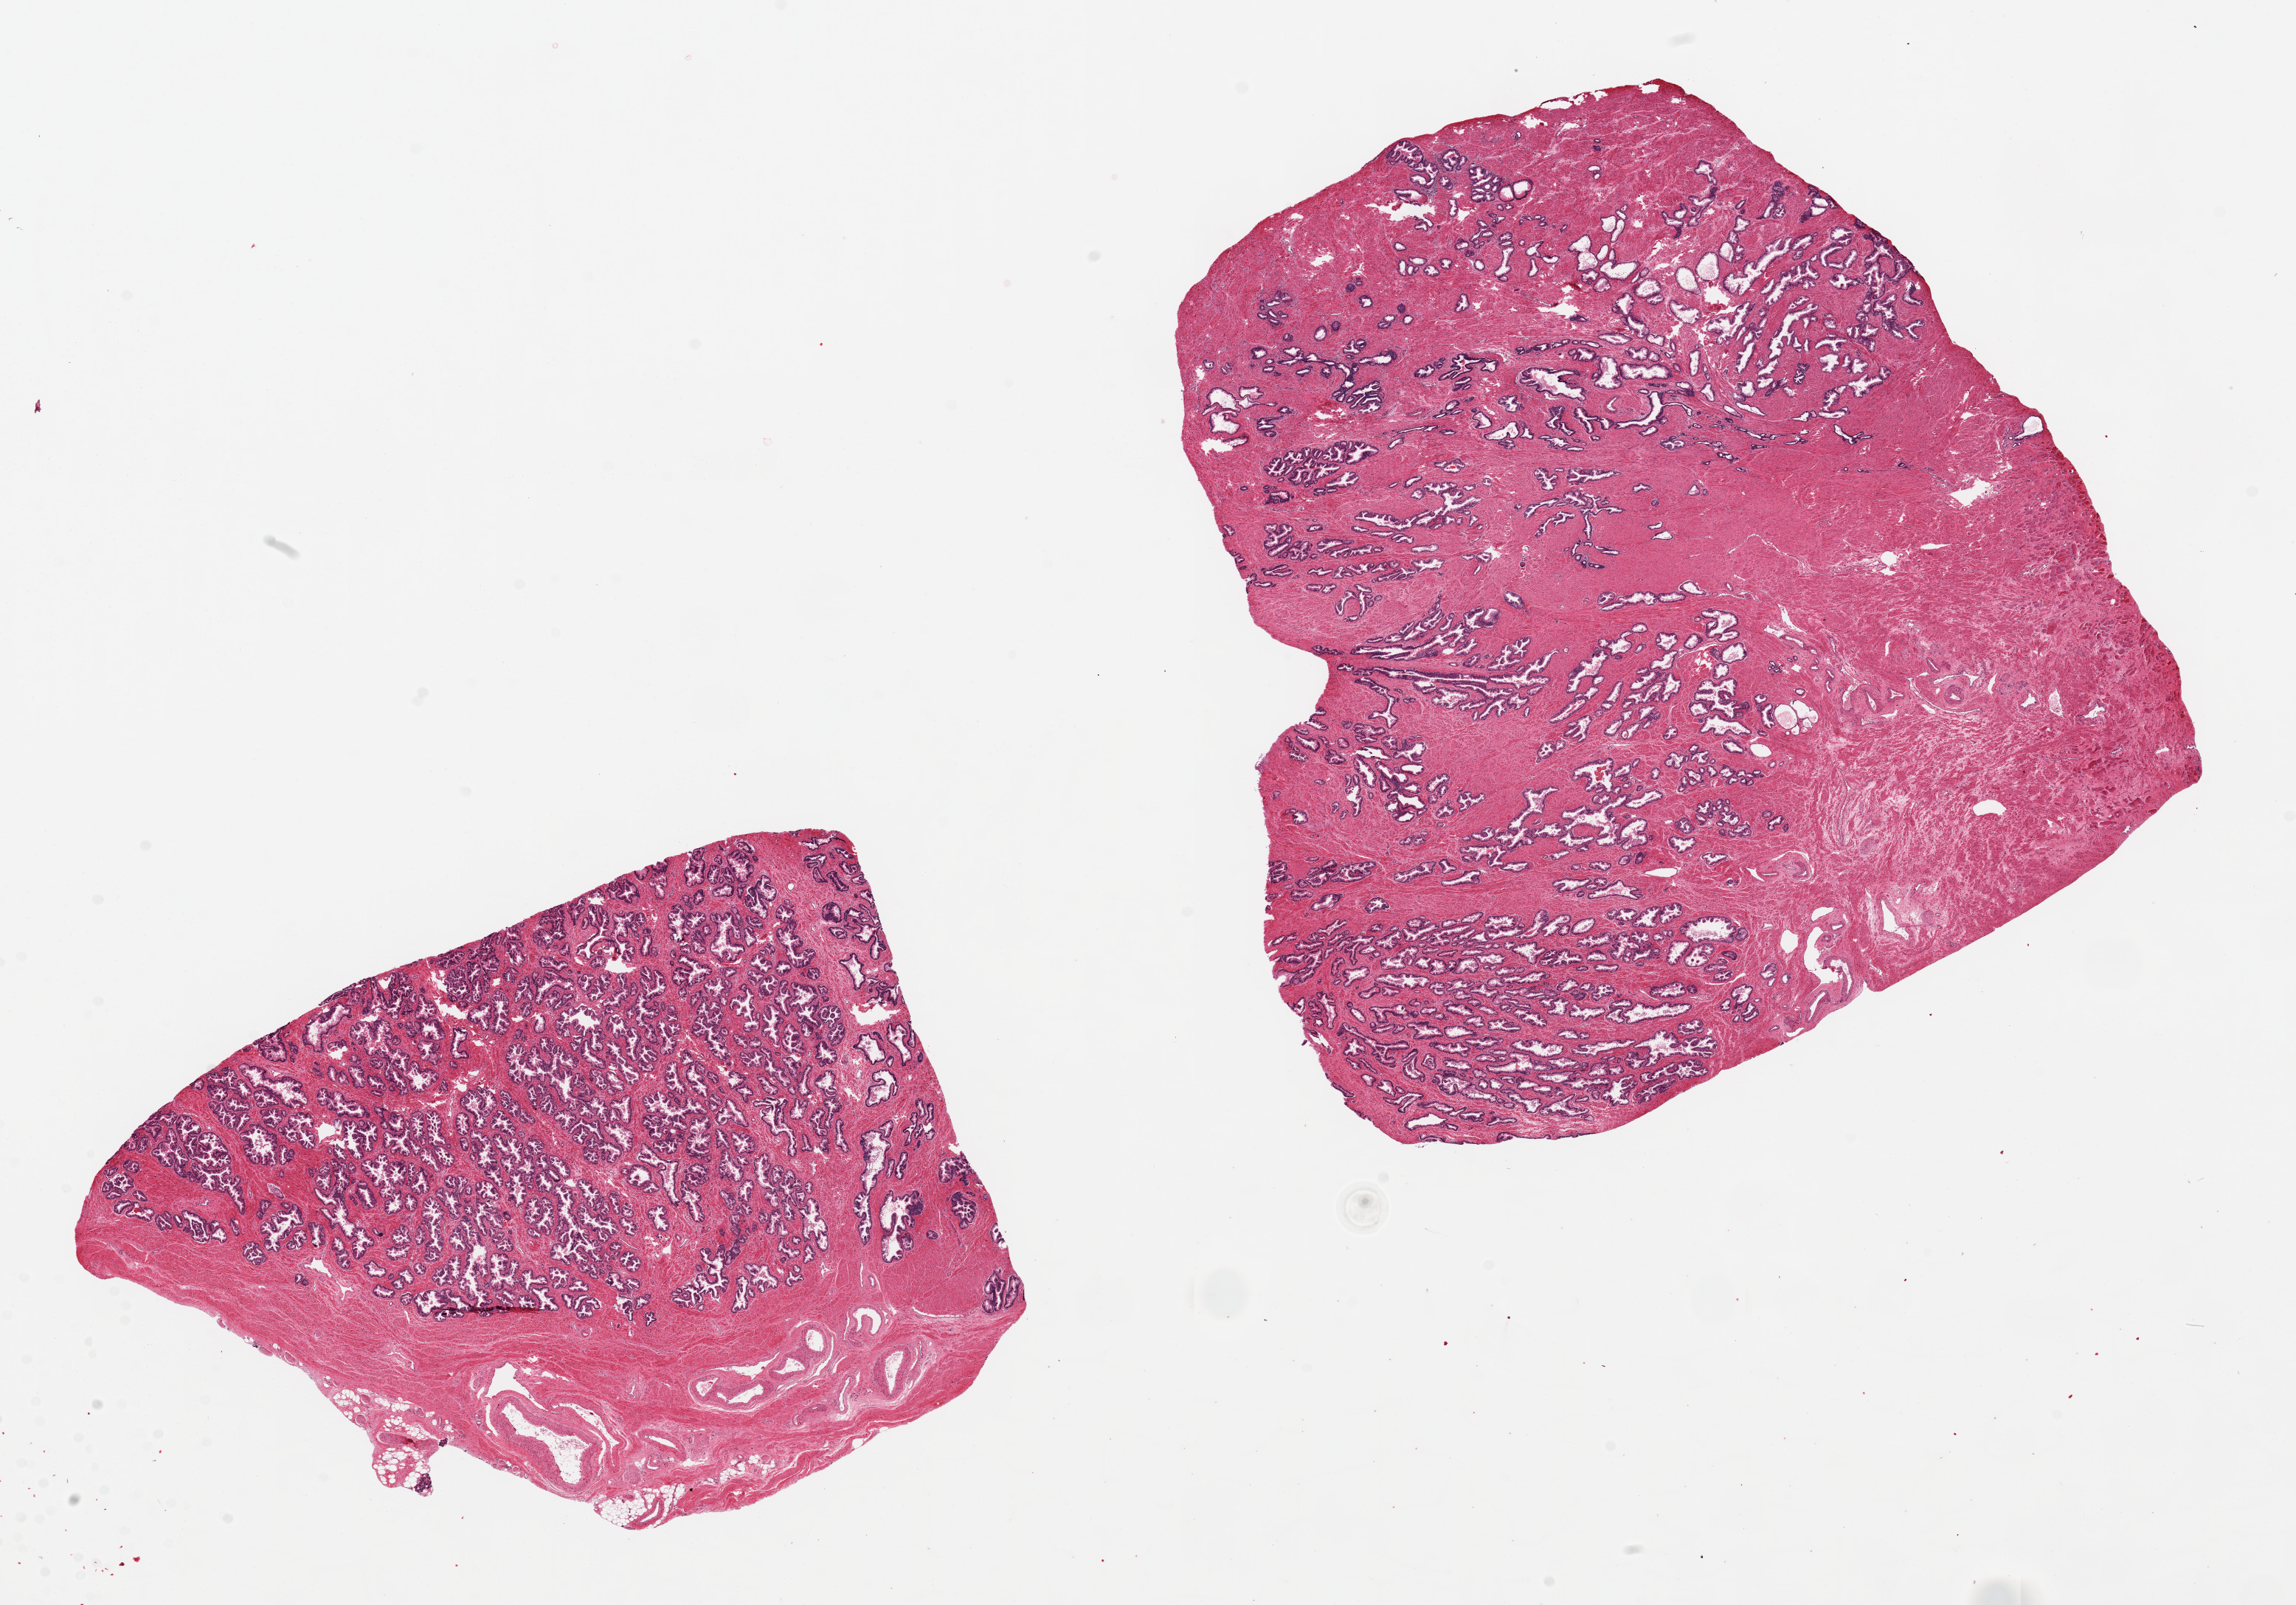
Digitized H&E-stained section, brightfield, shown as a low-resolution overview of the whole scanned area (about 24.6 x 17.2 mm, acquisition: 20x scan). PAXgene-fixed, paraffin-embedded tissue. Section of prostate (target tissue). Tissue donor sample.
Pathologist's review note for this sample: 2 ~10x10 & 9 x 6mm; focal atrophy.